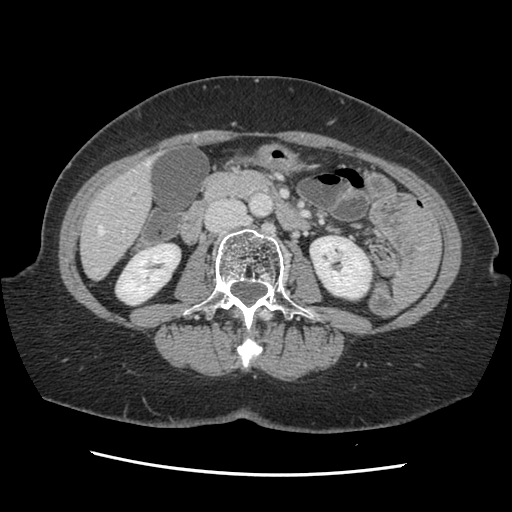
Contrast-enhanced abdominal CT, one axial slice; slice 44 of 141 in the series (ordered by position); 120 kVp; soft-tissue window (W 400 / L 40 HU); 512 × 512 image matrix. Female patient, age 61 years. Case-level facts recorded for this patient, not image findings: diagnosis: colorectal cancer liver metastases, imaged before liver resection; multiple liver metastases: no; largest metastasis: 2.4 cm; disease in both lobes: no.
Outlined on this slice (expert manual segmentation):
- hepatic veins: box from (x=95, y=162) to (x=149, y=272) px
- liver: (x=82, y=164)–(x=152, y=278)
- planned liver remnant (the part of the liver to remain after resection): (x=82, y=176)–(x=152, y=278)